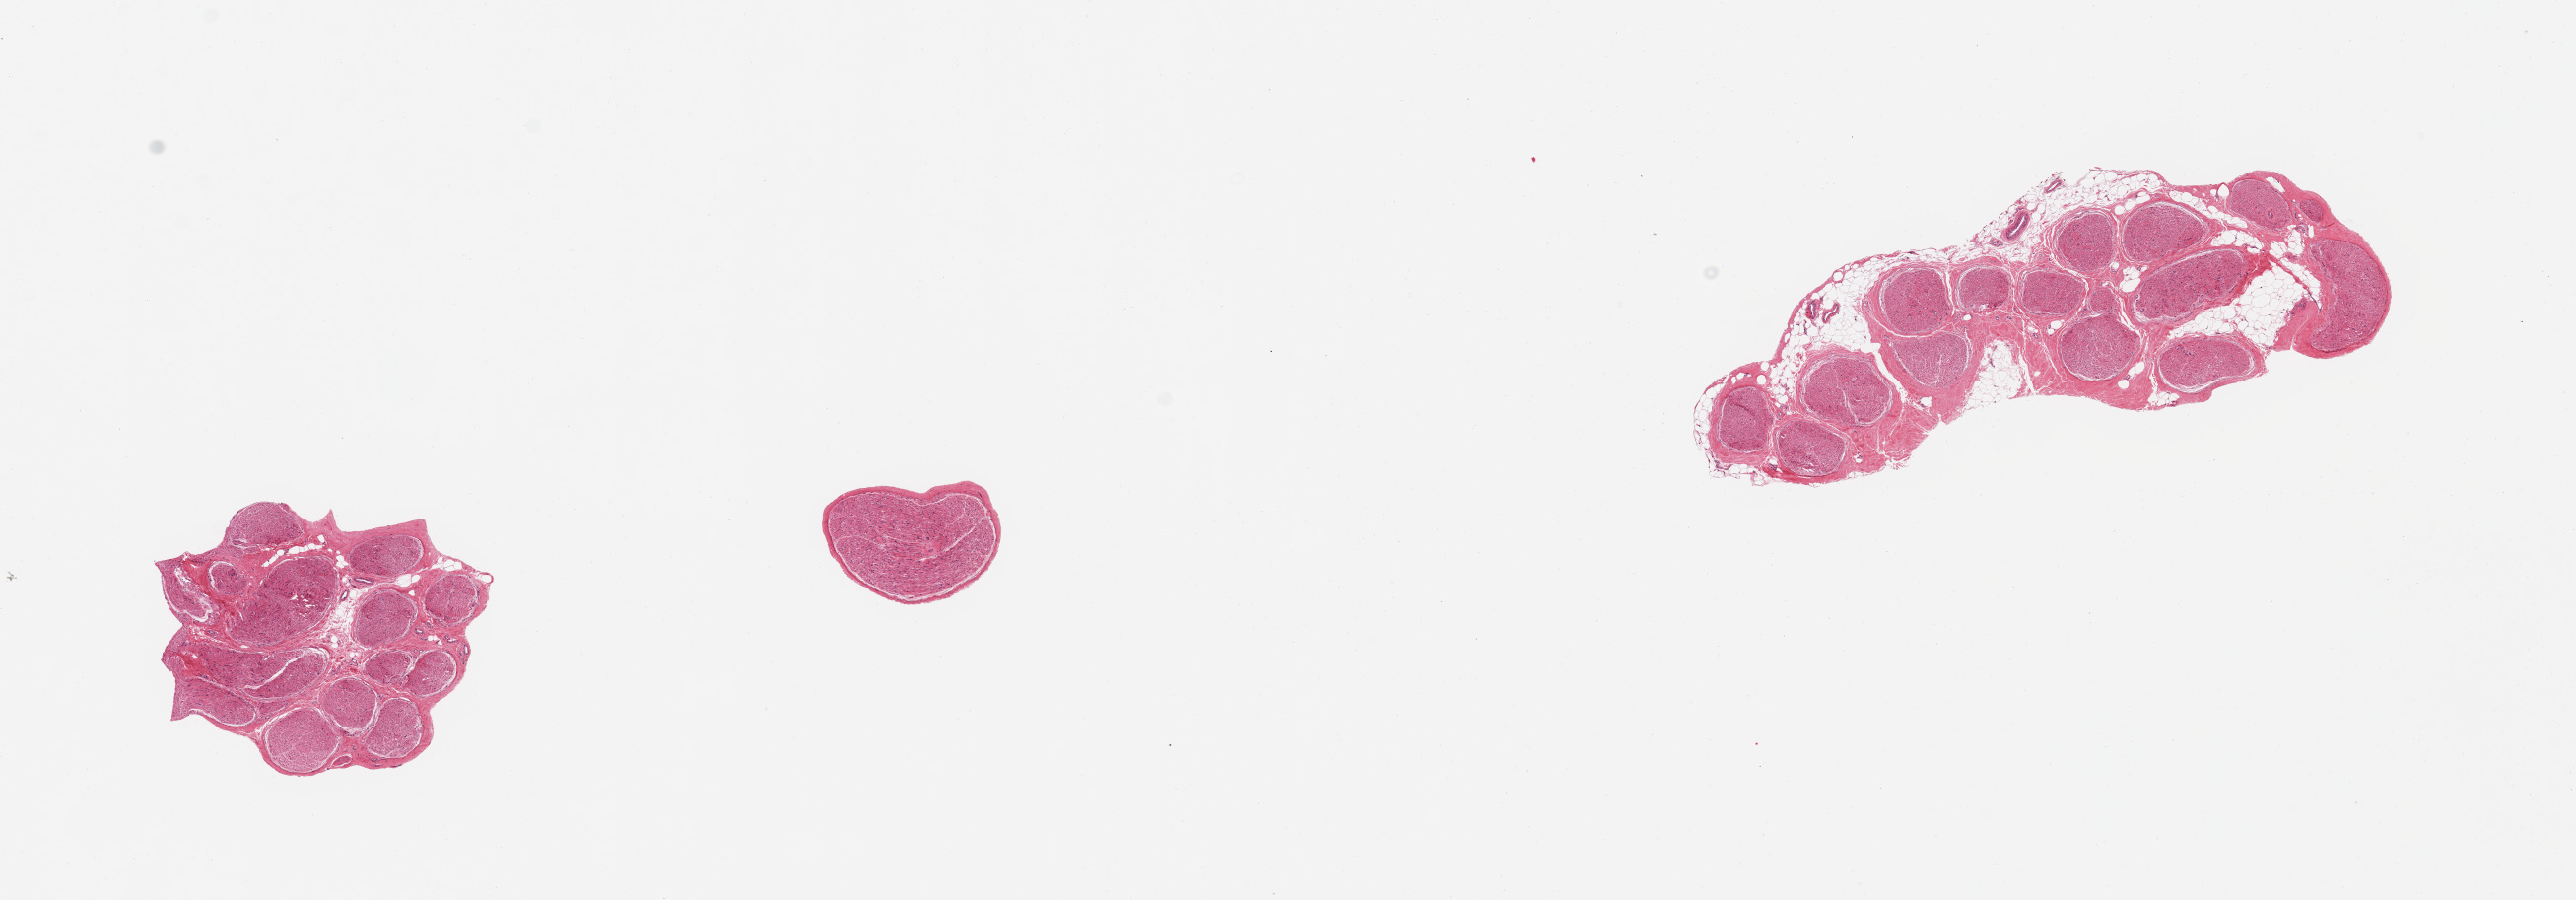
Digitized H&E-stained section, brightfield, low-resolution overview of the scanned area, about 20.7 x 7.2 mm; PAXgene-fixed paraffin-embedded (PFPE) section; sampled site (target tissue): tibial nerve; tissue donor sample. Donor sex: female.
Review note (as recorded): 3 pieces; 1 piece includes ~15% fat (attached and internal).